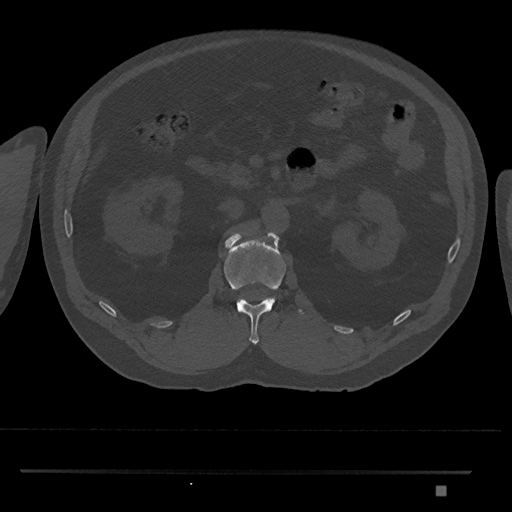
CT including the spine, one axial slice. Position 811 of 1134 along the scan axis. 120 kVp. Bone window (W 1800 / L 400 HU). 512 × 512 image matrix. Male patient, age 65 years. Case-level facts recorded for this patient, not image findings: primary cancer: prostate.
Annotated regions visible in this slice (semi-automatic segmentation, software-assisted and operator-edited):
- L1 vertebra: bounding box (x1, y1, x2, y2) in pixels: (223, 230, 304, 344)